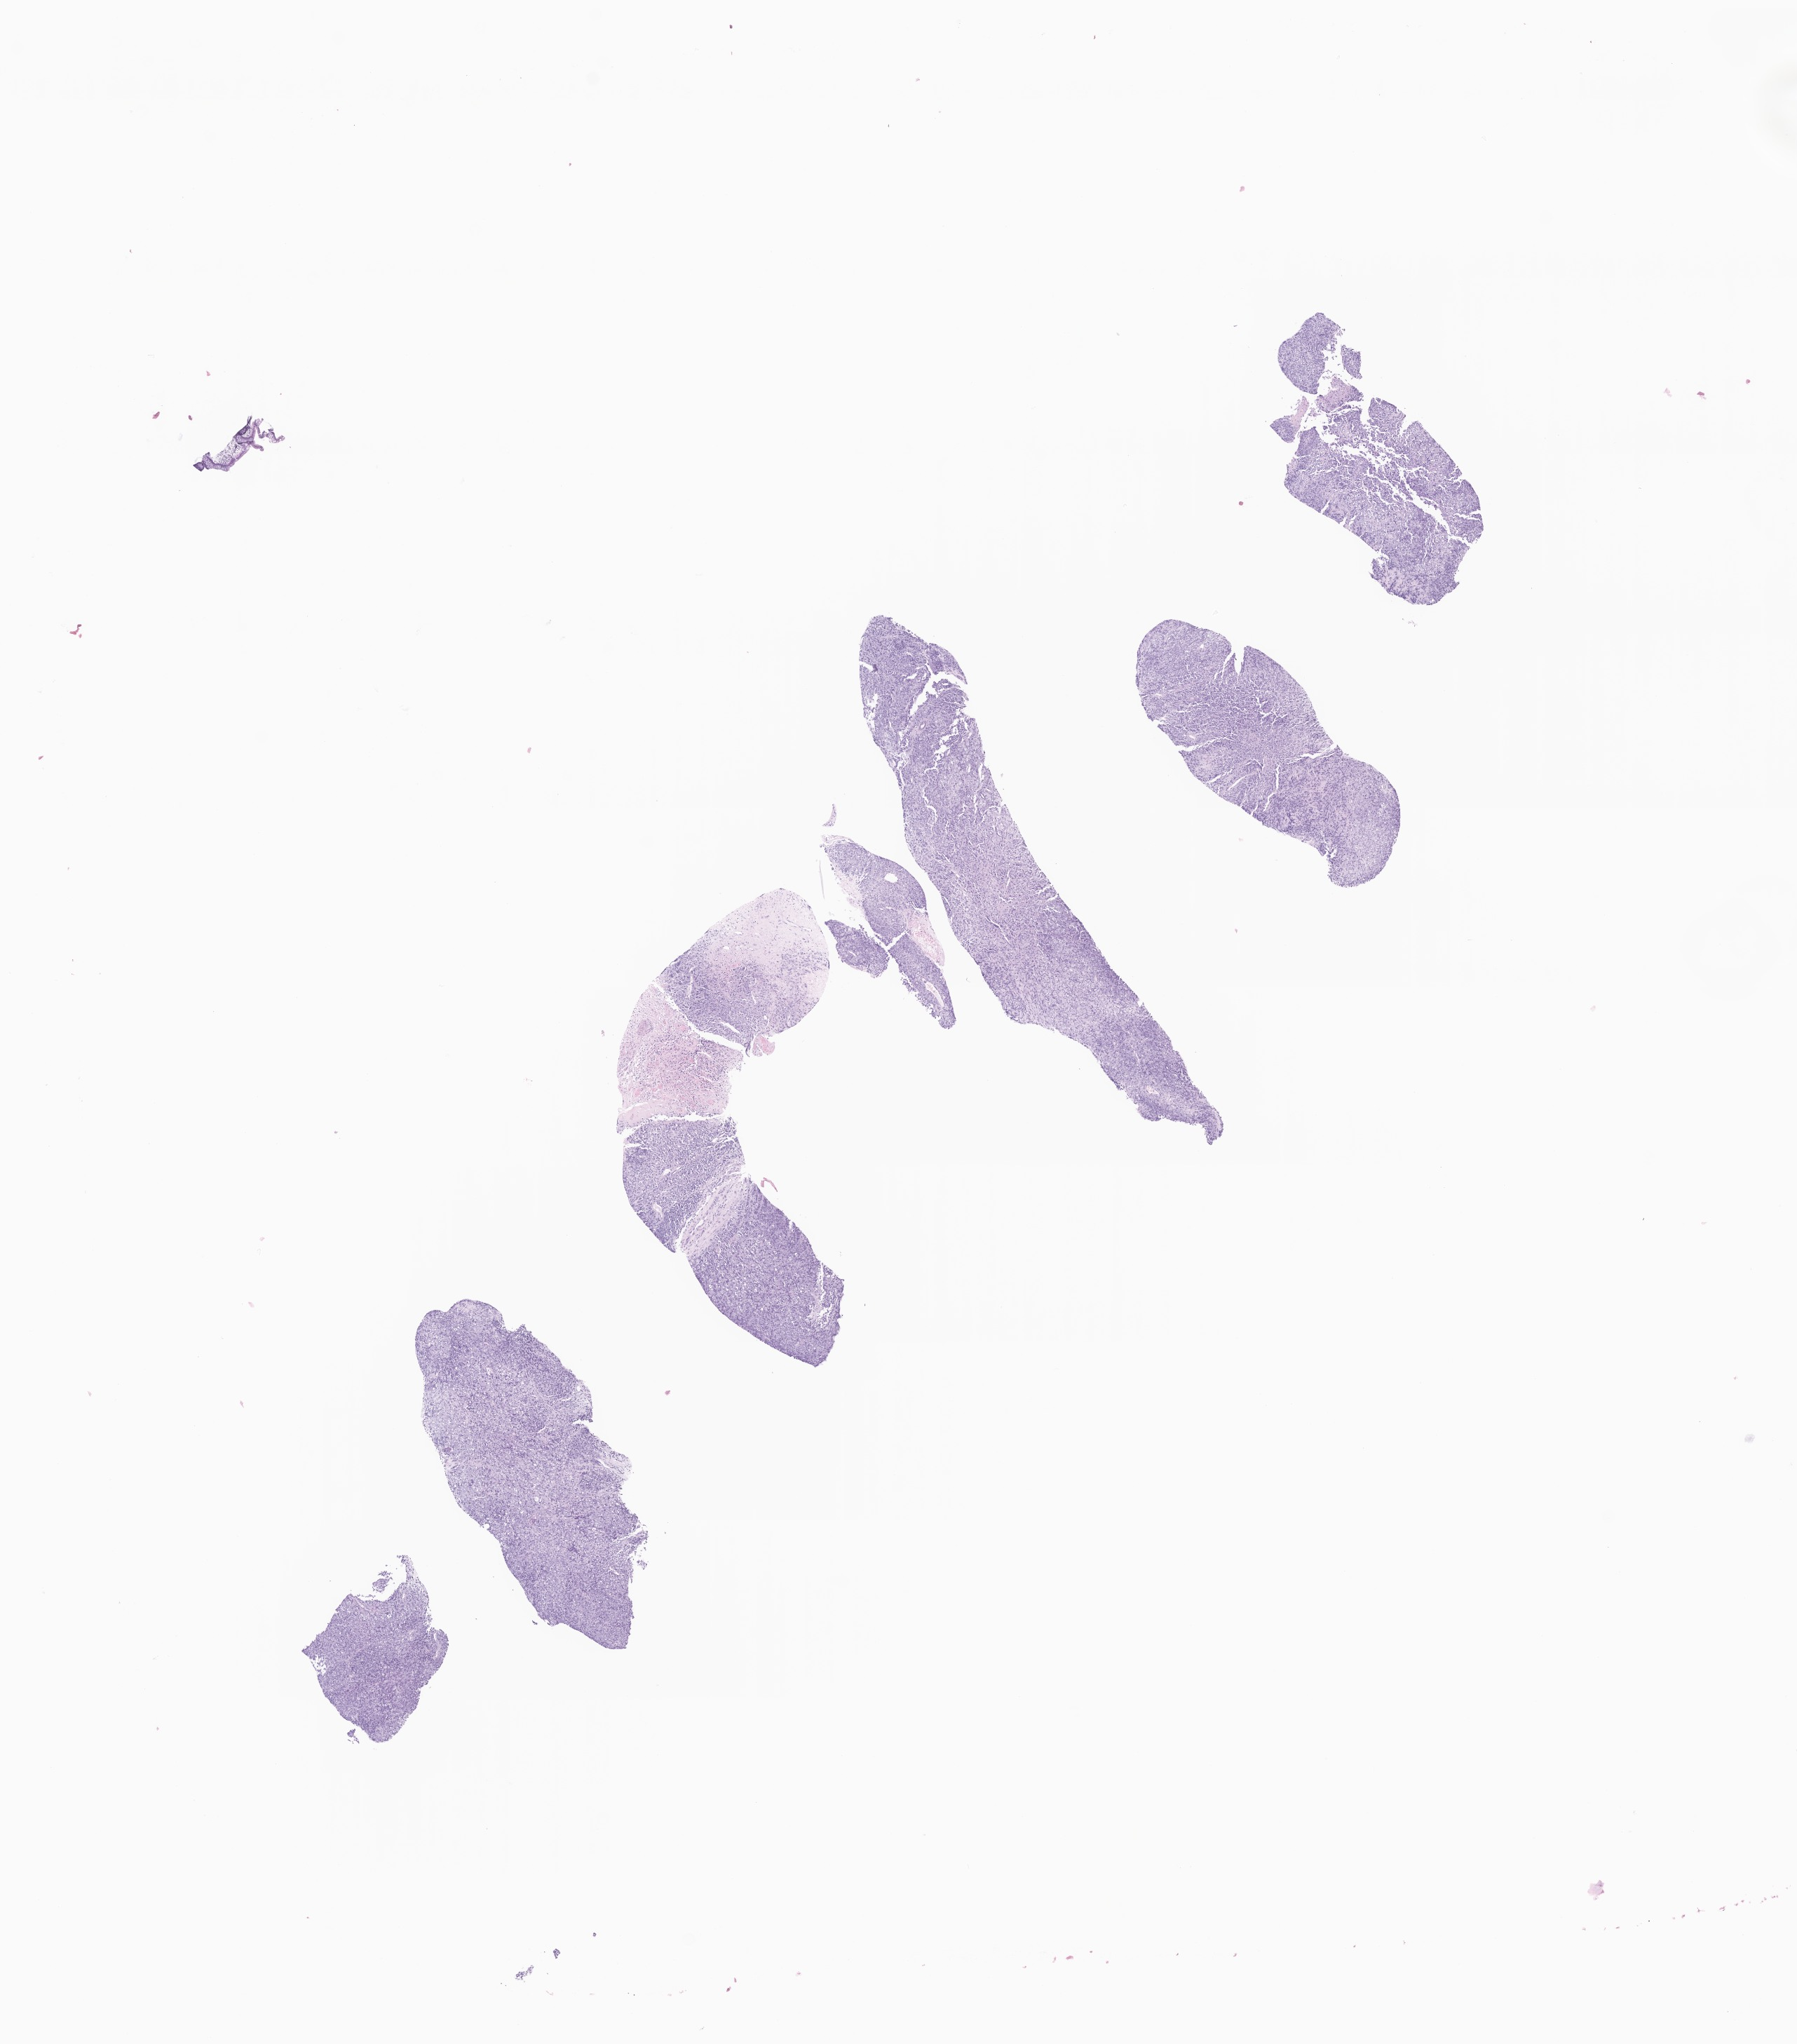
Digitized hematoxylin and eosin (H&E)-stained section of tumor tissue from the brain, low-resolution overview of the scanned area, about 10.8 x 12.3 mm, FFPE section. Patient male; age 257 days.
Recorded diagnosis: Neoplasm, malignant.